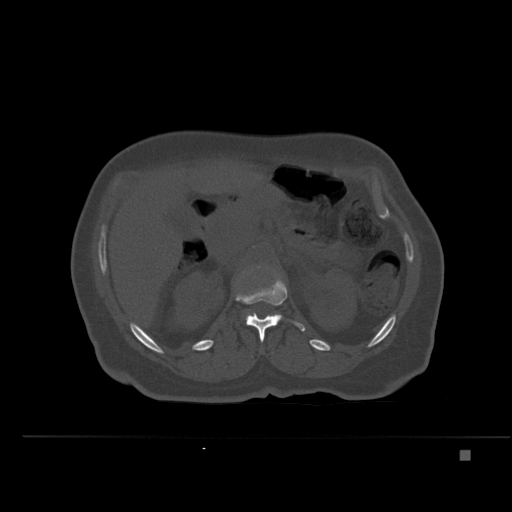
CT including the spine, one axial slice. Slice 232 of 477 in the series (ordered by position). Bone window (W 1800 / L 400 HU). 1.5 mm slice thickness. 512 × 512 image matrix, field of view 422 × 422 mm. Female patient, age 74 years. Case-level facts recorded for this patient, not image findings: primary cancer: colon.
Structures marked on this image (semi-automatic segmentation, software-assisted and operator-edited):
- L1 vertebra: bounding box (x1, y1, x2, y2) in pixels: (236, 275, 305, 342)
- L2 vertebra: (245, 314, 250, 320)